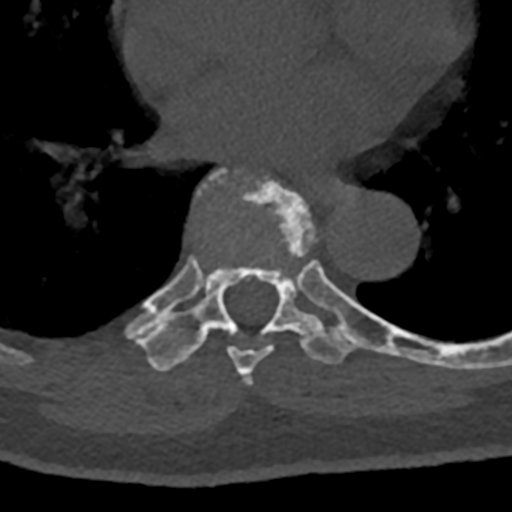
CT including the spine, one axial slice. Position 732 of 797 along the scan axis. 120 kVp. Bone window (W 1800 / L 400 HU). 0.5 mm slice thickness. 512 × 512 image matrix, field of view 160 × 160 mm. Patient: male, 74 years. Case-level facts recorded for this patient, not image findings: primary cancer: renal; vertebrae with lytic lesions (as recorded): T10, L1, L2, L3, L4, L5.
Structures marked on this image (semi-automatic segmentation, software-assisted and operator-edited):
- T7 vertebra: bounding box [x1, y1, x2, y2] px = [201, 169, 355, 384]
- T8 vertebra: [128, 267, 432, 372]